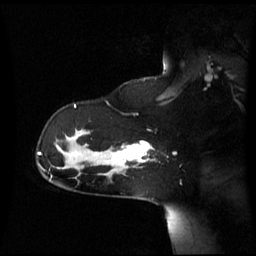
Breast MRI (dynamic contrast-enhanced), one sagittal slice; slice 44 of 60 in the series (ordered by position); dynamic contrast-enhanced series, image 2 of 3 at this slice position (ordered by acquisition); 1.5 T; TE 4.2 ms, TR 8.4 ms; 2.8 mm slice thickness; 256 × 256 image matrix, field of view 270 × 270 mm. Patient: female, 39 years. From the clinical record (not read from this slice): setting: breast cancer imaged before/during neoadjuvant chemotherapy; receptor status: triple-negative.
Annotated regions visible in this slice (semi-automatically segmented with operator editing):
- analysis volume of interest (the breast-tissue region the enhancement analysis was run in; not a lesion): bounding box [x1, y1, x2, y2] px = [101, 141, 150, 173]
- tumour enhancement mask (voxels above the 70 % enhancement threshold inside the analysis volume of interest): [112, 142, 150, 165]